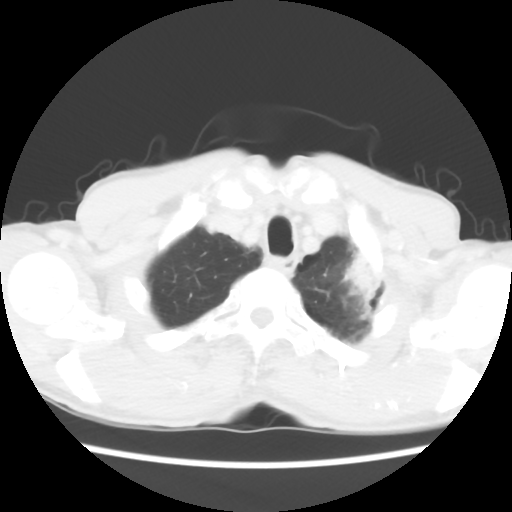
Chest CT, one axial slice. Position 54 of 60 along the scan axis. Reconstruction kernel STANDARD. 120 kVp. Lung window (W 1500 / L -600 HU). 5 mm slice thickness. 512 × 512 image matrix, field of view 308 × 308 mm. Patient: male, 64 years. Case-level facts recorded for this patient, not image findings: clinical TNM (as recorded): T3 N3 M0; histopathological grade: G3.
Annotated regions visible in this slice (rectangle marked by the reading radiologist):
- lung tumour (recorded histology: adenocarcinoma): box from (x=342, y=250) to (x=384, y=318) px